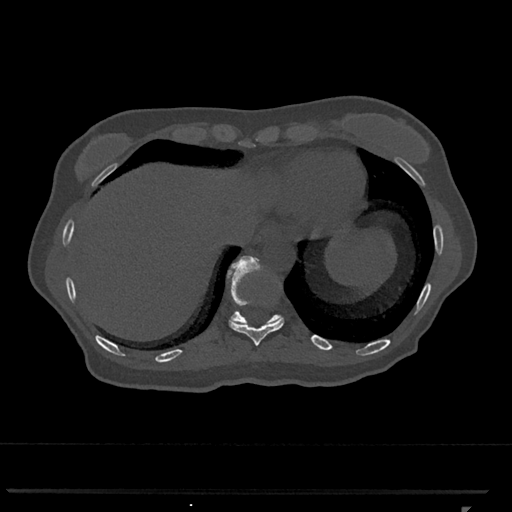
CT including the spine, one axial slice. Slice 555 of 793 in the series (ordered by position). Bone window (W 1800 / L 400 HU). 512 × 512 image matrix. Female patient, age 62 years. Case-level facts recorded for this patient, not image findings: primary cancer: renal.
Structures marked on this image (semi-automatically segmented with operator editing):
- T10 vertebra: box from (x=229, y=273) to (x=285, y=346) px
- T11 vertebra: (x=227, y=256)–(x=282, y=325)